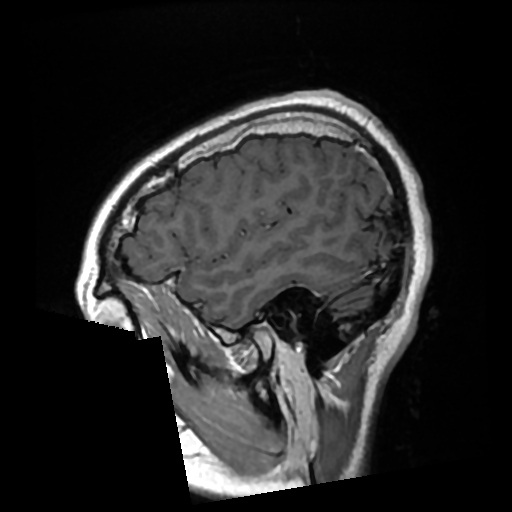
Brain MRI from a brain-tumour surgery series, one sagittal slice; slice 70 of 276 in the series (ordered by position); T1-weighted post-contrast; 512 × 512 image matrix, field of view 250 × 250 mm. Case-level facts recorded for this patient, not image findings: histopathology: Glioma with ependymal features; WHO grade: 2.
Outlined on this slice (outlined manually by an expert reader):
- previous resection cavity: bounding box (x1, y1, x2, y2) in pixels: (387, 231, 391, 241)